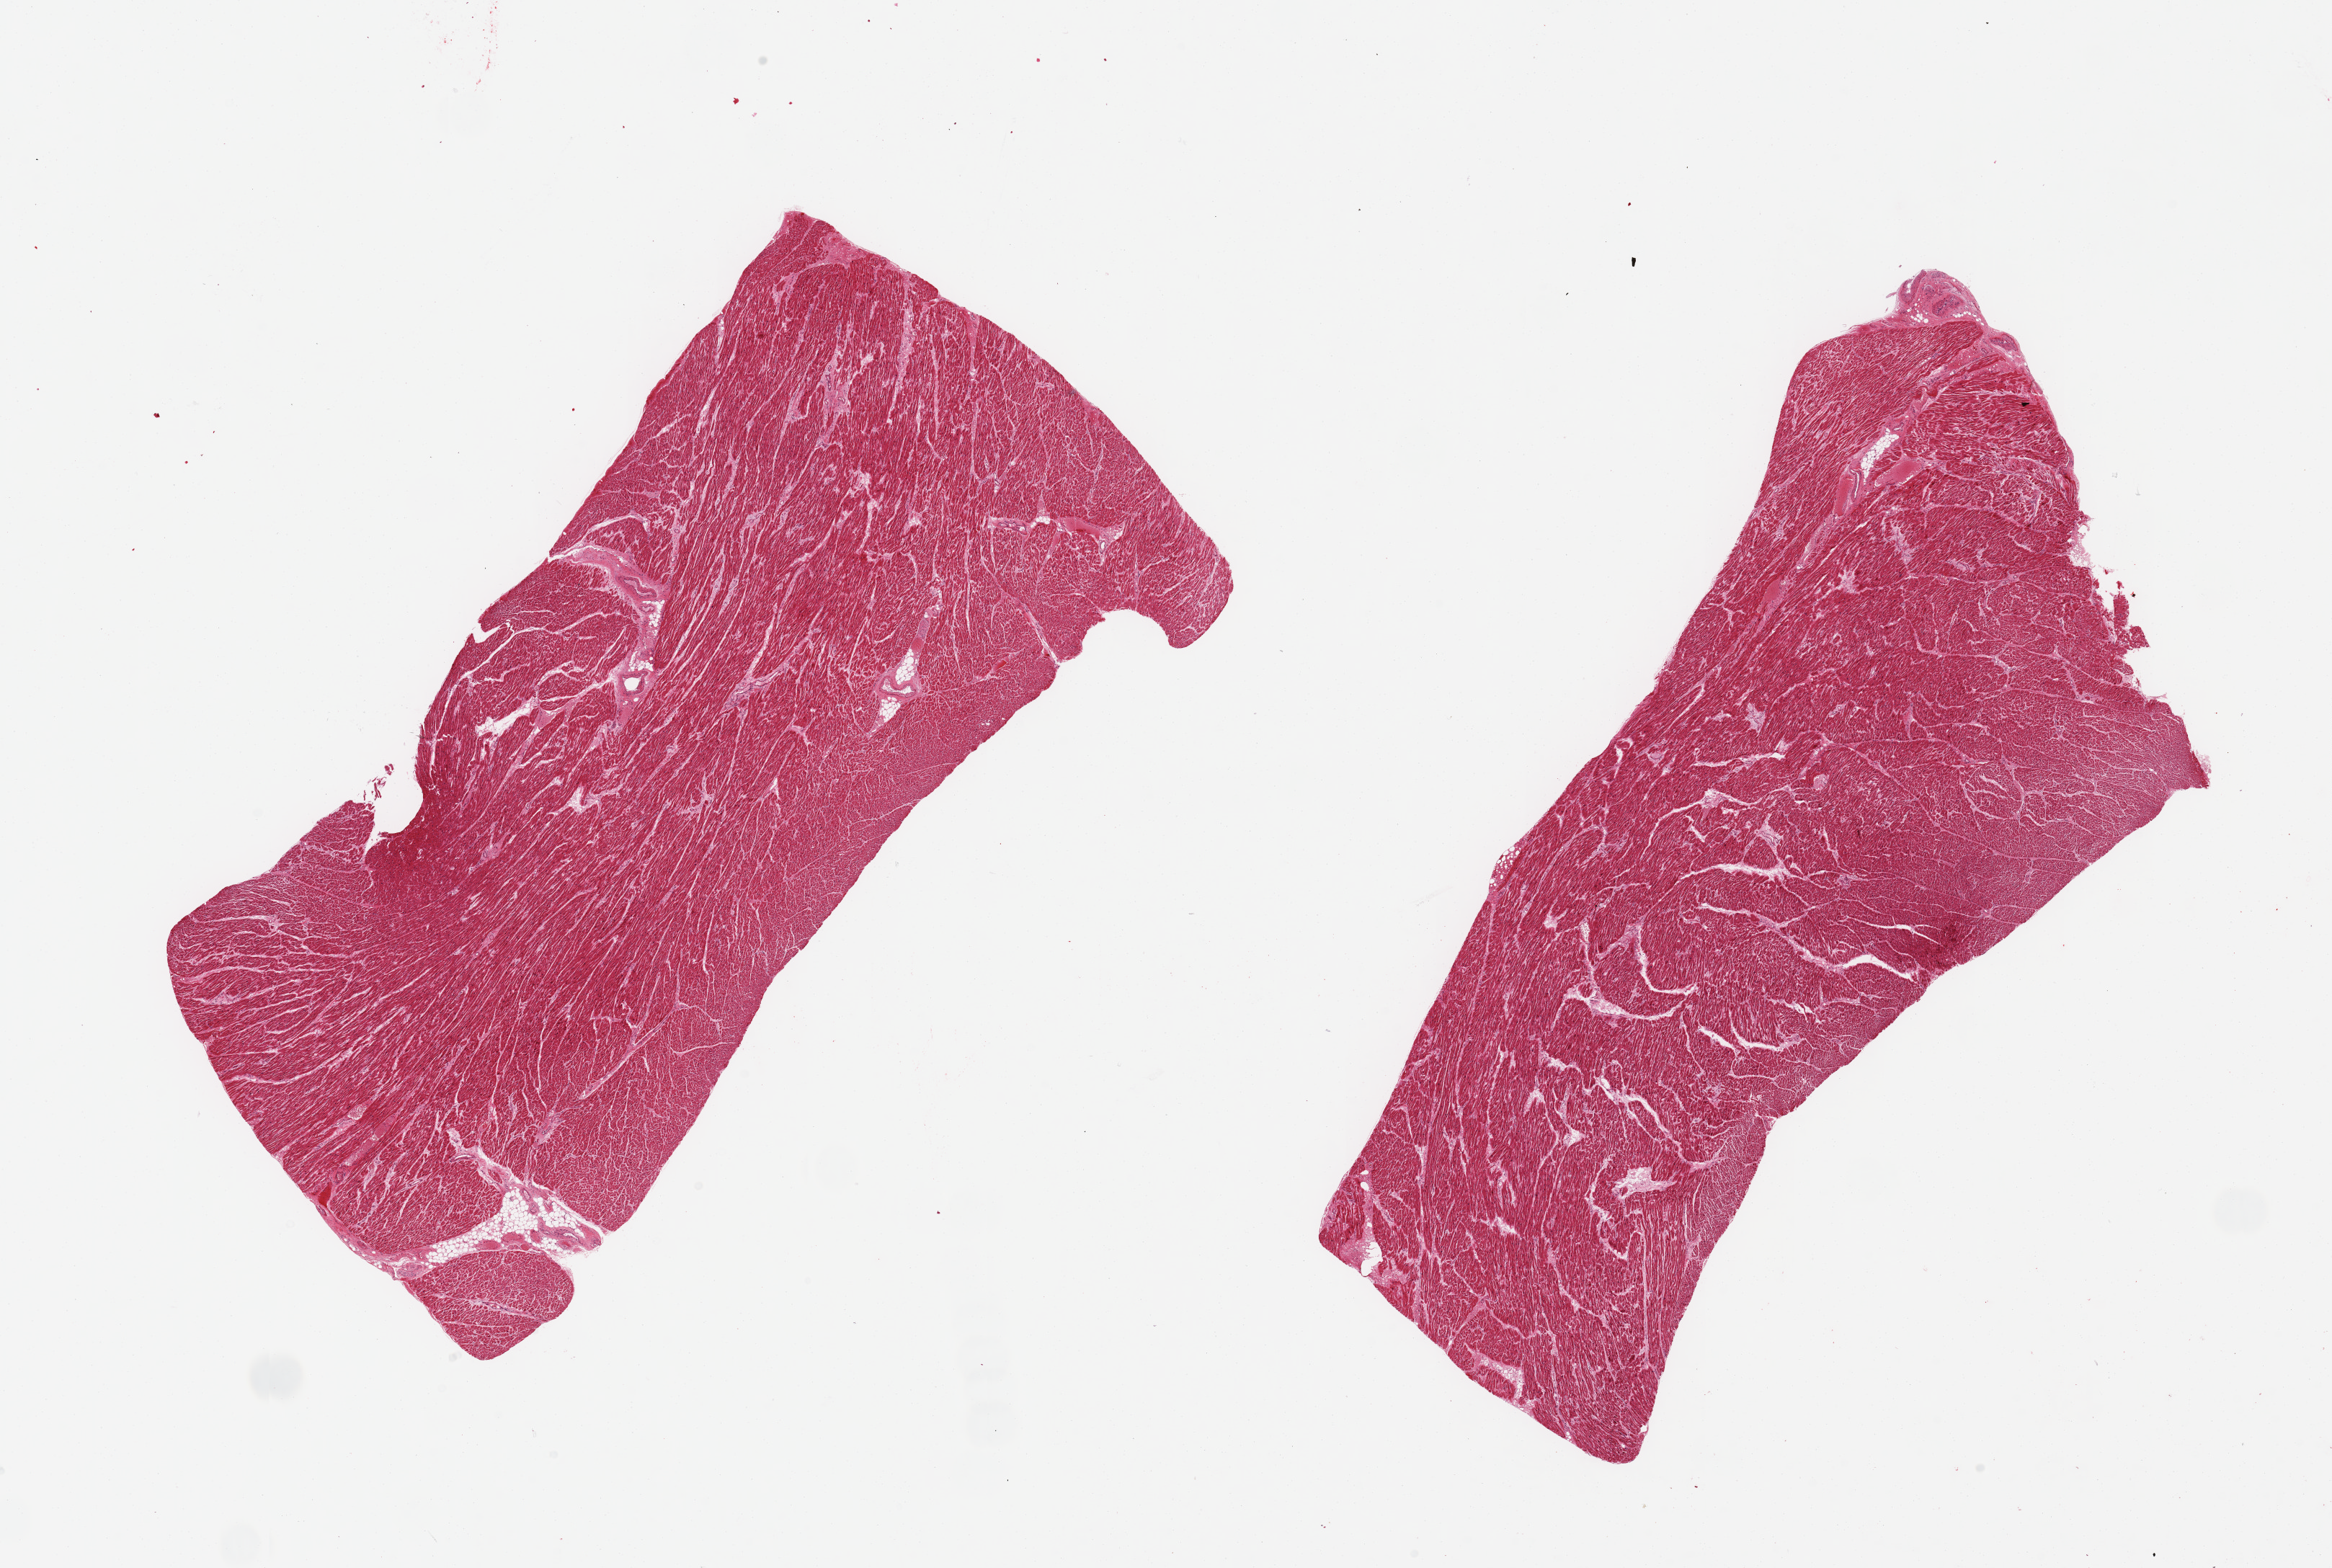
Hematoxylin and eosin (H&E) whole-slide image — a low-resolution overview of the entire scanned area, about 25.6 x 17.2 mm. PAXgene-fixed, paraffin-embedded tissue. Sampled site (target tissue): heart. Tissue donor sample.
• pathologist's review note for this sample: 2 pieces